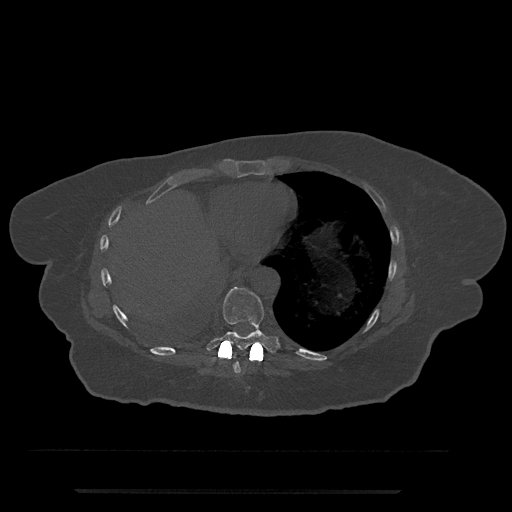
CT including the spine, one axial slice; position 340 of 797 along the scan axis; bone window (W 1800 / L 400 HU); 0.5 mm slice thickness; 512 × 512 image matrix, field of view 440 × 440 mm. Patient: female, 51 years. Case-level facts recorded for this patient, not image findings: primary cancer: neuro.
Structures marked on this image (semi-automatically segmented with operator editing):
- T8 vertebra: box from (x=234, y=353) to (x=241, y=373) px
- T9 vertebra: (x=206, y=287)–(x=278, y=358)